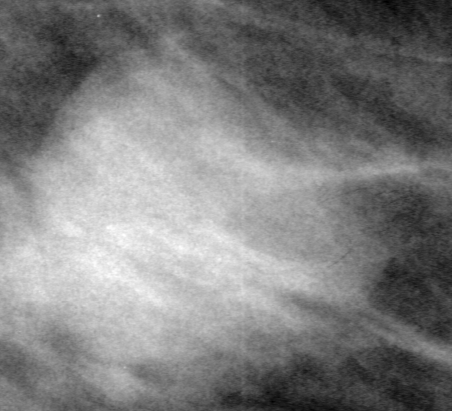
Crop from a digitized film mammogram around one marked abnormality; right breast; MLO view.
Finding: mass, shape lobulated, margins circumscribed; BI-RADS assessment category 4; pathology result (as recorded, not read from the image): benign.